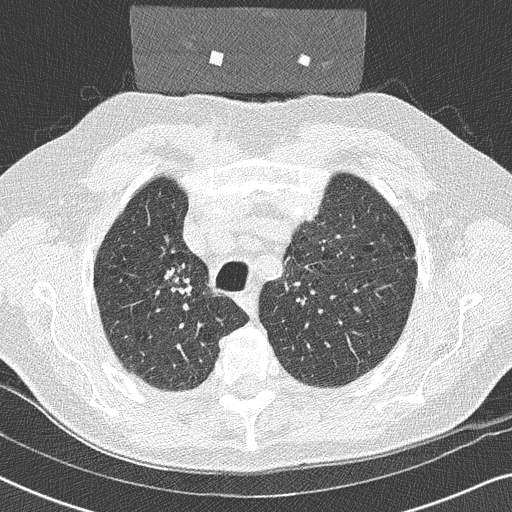
Axial slice from a low-dose chest CT screening exam. Second annual screen. Lung window (W 1500 / L -600 HU). 2 mm slice thickness. 512 × 512 image matrix, field of view 330 × 330 mm. Male, age 59 years at enrolment. Former smoker at enrolment.
Lesion marked by an expert reader, bounding box <156,260,210,308> (left, top, right, bottom; pixels). The exam's reader record, not a measurement of the box and not confirmed to be the same lesion: non-calcified nodule or mass ≥4 mm, right upper lobe, 17 × 16 mm, smooth margins, soft tissue attenuation, pre-existing on the prior screen: yes. Official screen result: positive, other. Later outcome: lung cancer diagnosed 14 days after this screen — squamous cell carcinoma, NOS, right upper lobe, poorly differentiated (G3), stage IIA (AJCC 6th edition), 20 mm at pathology.